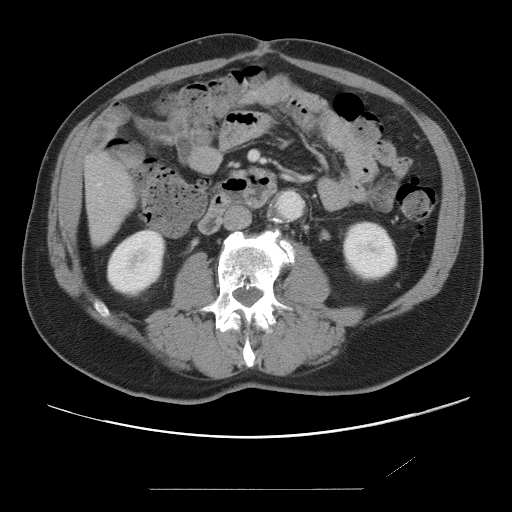
Contrast-enhanced abdominal CT, one axial slice. Slice 14 of 87 in the series (ordered by position). Intravenous contrast given. Soft-tissue window (W 400 / L 40 HU). 512 × 512 image matrix. Male patient, age 74 years. Case-level facts recorded for this patient, not image findings: diagnosis: colorectal cancer liver metastases, imaged before liver resection; multiple liver metastases: yes; largest metastasis: 1.1 cm; disease in both lobes: no.
Structures marked on this image (expert manual segmentation):
- hepatic veins: bounding box (x1, y1, x2, y2) in pixels: (98, 183, 101, 186)
- liver: (86, 154, 133, 245)
- planned liver remnant (the part of the liver to remain after resection): (85, 154, 133, 245)